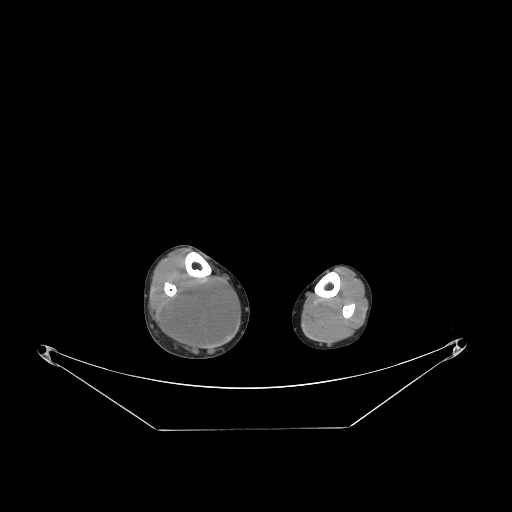
CT of an extremity soft-tissue mass (from a PET/CT study), one axial slice. Position 80 of 267 along the scan axis. Reconstruction kernel STANDARD. 140 kVp. Soft-tissue window (W 400 / L 40 HU). 3.75 mm slice thickness. 512 × 512 image matrix. Male patient. From the clinical record (not read from this slice): histological type: liposarcoma - round cell; grade: high; site of the primary tumour: right calf.
Outlined on this slice (expert contour drawn on MRI and transferred to this co-registered scan by the dataset authors):
- gross tumour volume (mass): bounding box [x1, y1, x2, y2] px = [164, 279, 239, 346]